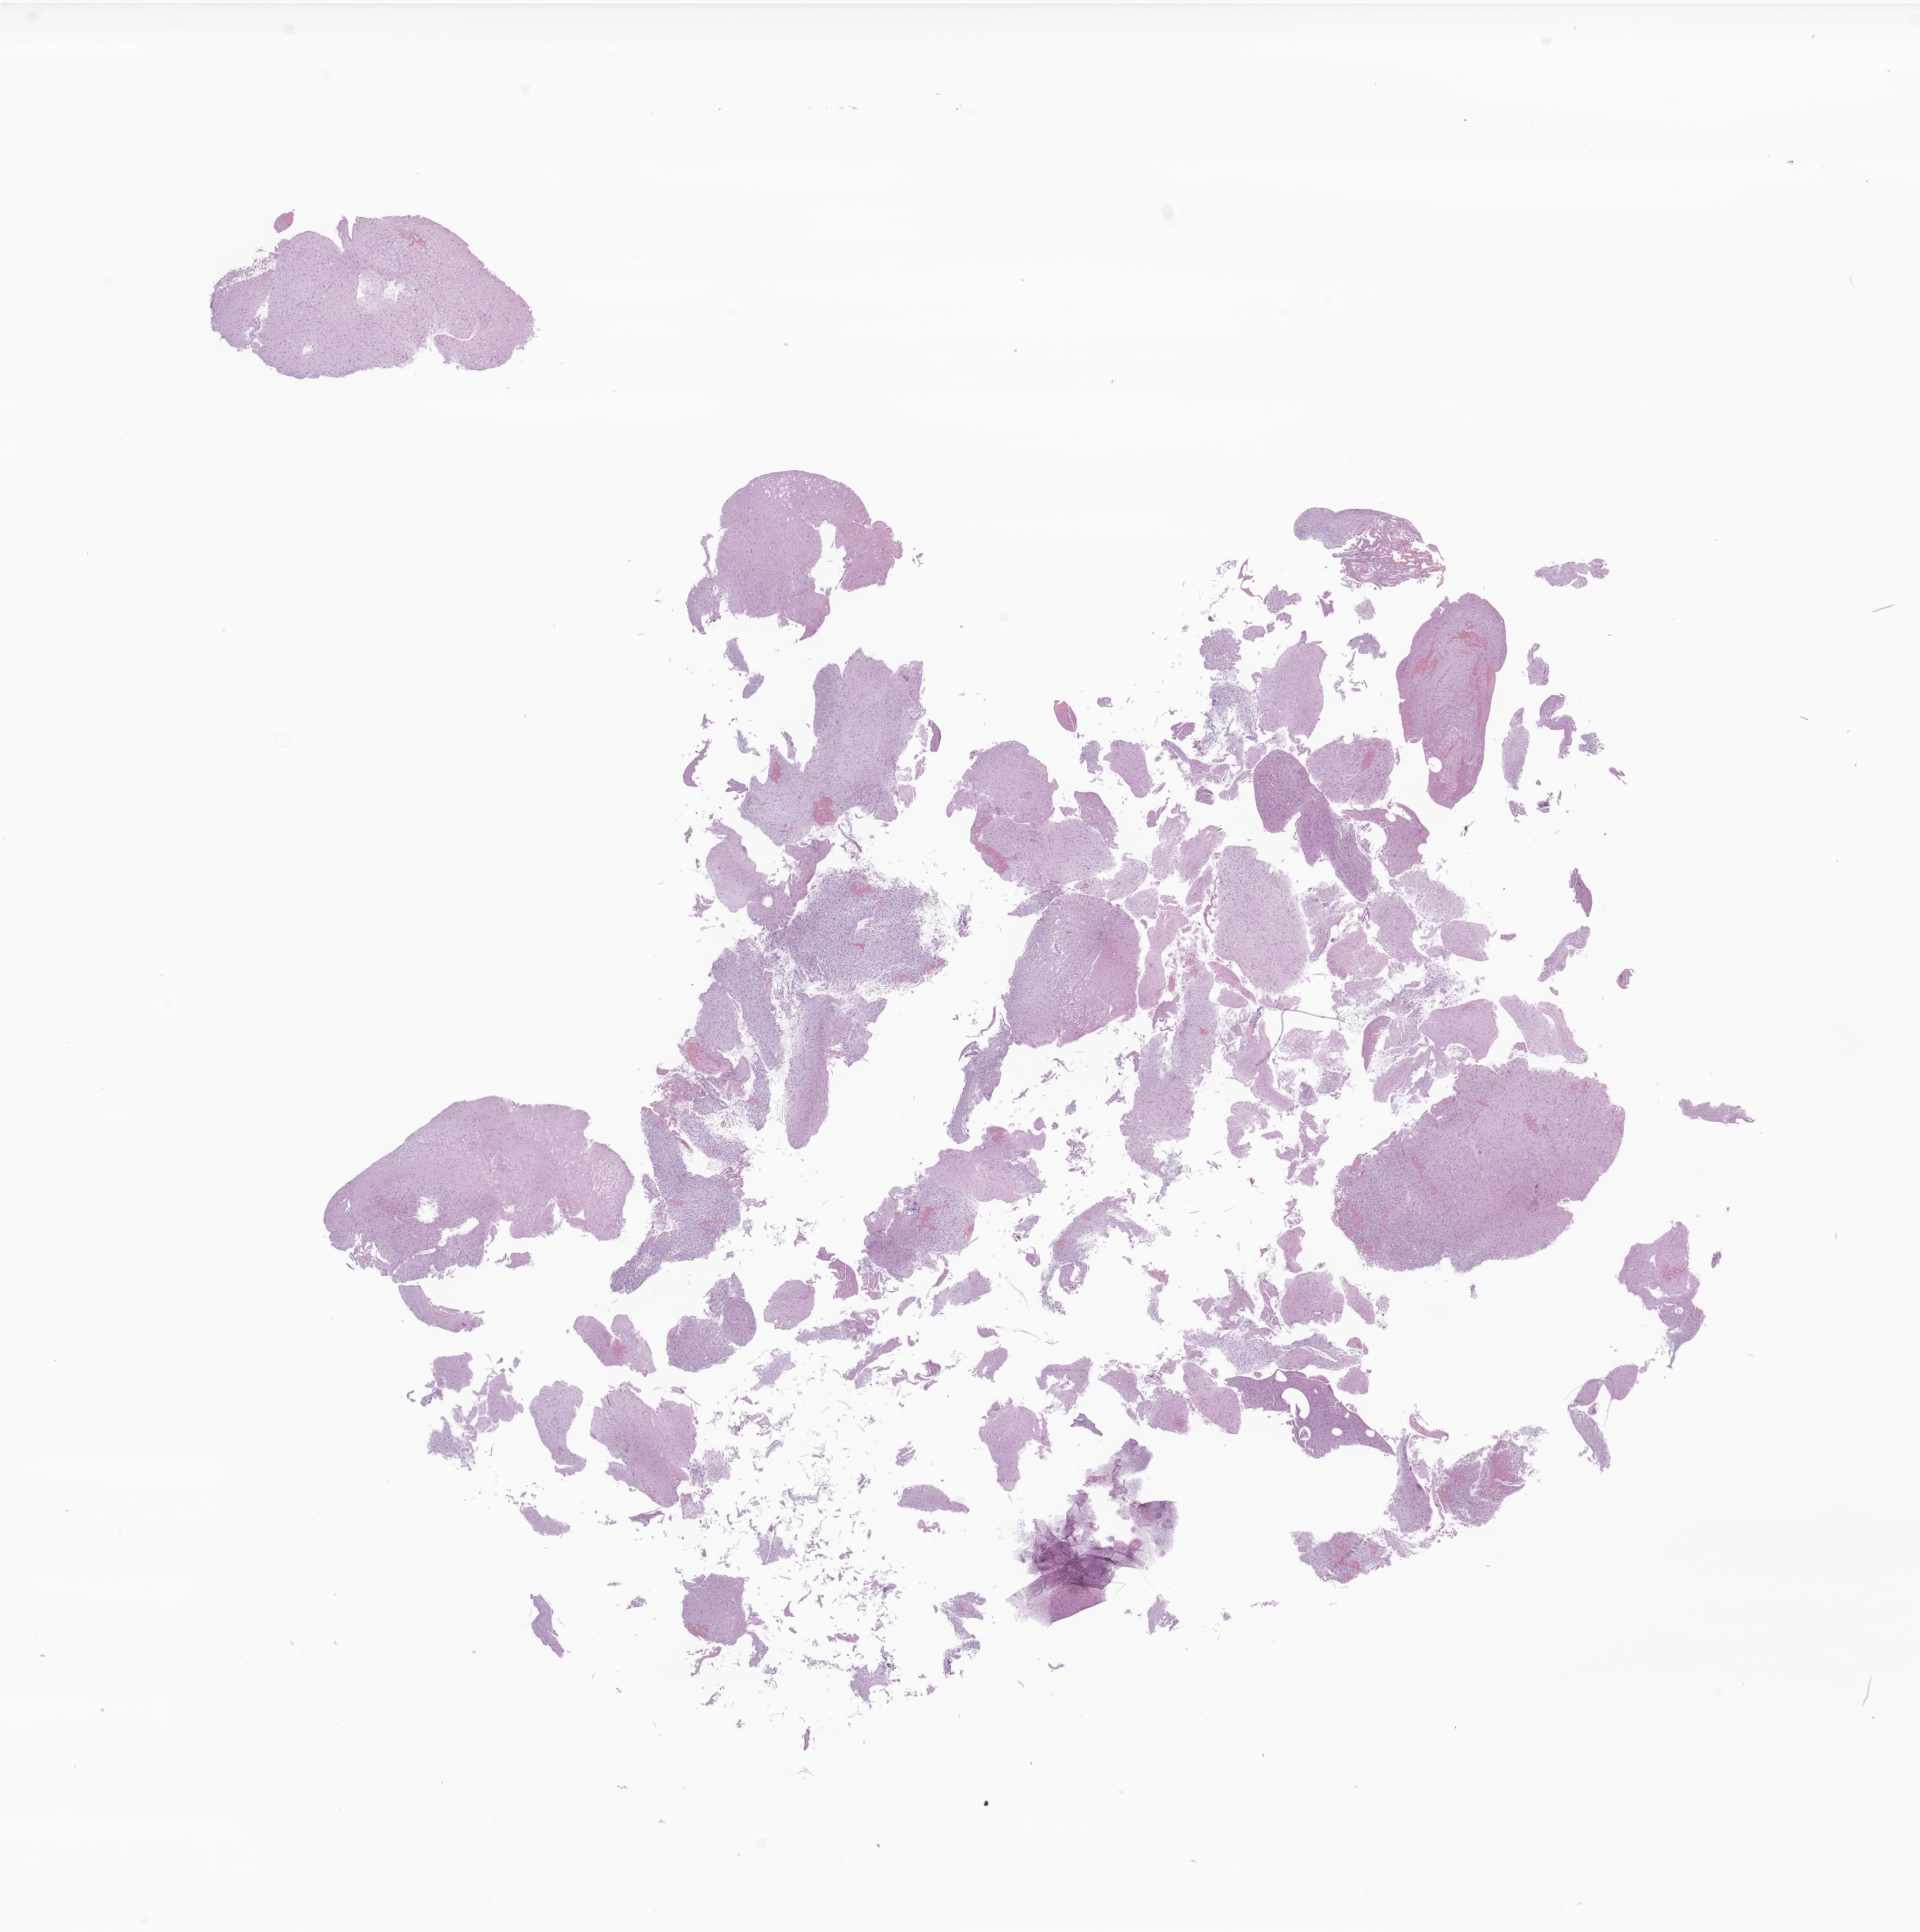
Whole-slide image, haematoxylin and eosin stain of tumor tissue from the brain, low-resolution overview of the scanned area, about 17.3 x 17.4 mm; FFPE section. Patient male; age 49 months (4 years 1 month).
Recorded diagnosis: Glioma, malignant.